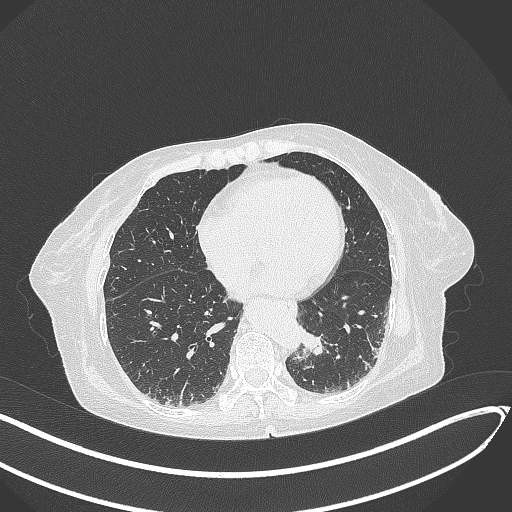
Chest CT, one axial slice; position 73 of 324 along the scan axis; reconstruction kernel B70f; 120 kVp; lung window (W 1500 / L -600 HU); 1 mm slice thickness; 512 × 512 image matrix. Female patient, age 82 years. From the clinical record (not read from this slice): clinical TNM (as recorded): T1b N0 M1.
Outlined on this slice (bounding box drawn by a radiologist):
- lung tumour (recorded histology: adenocarcinoma): box from (x=298, y=327) to (x=330, y=357) px